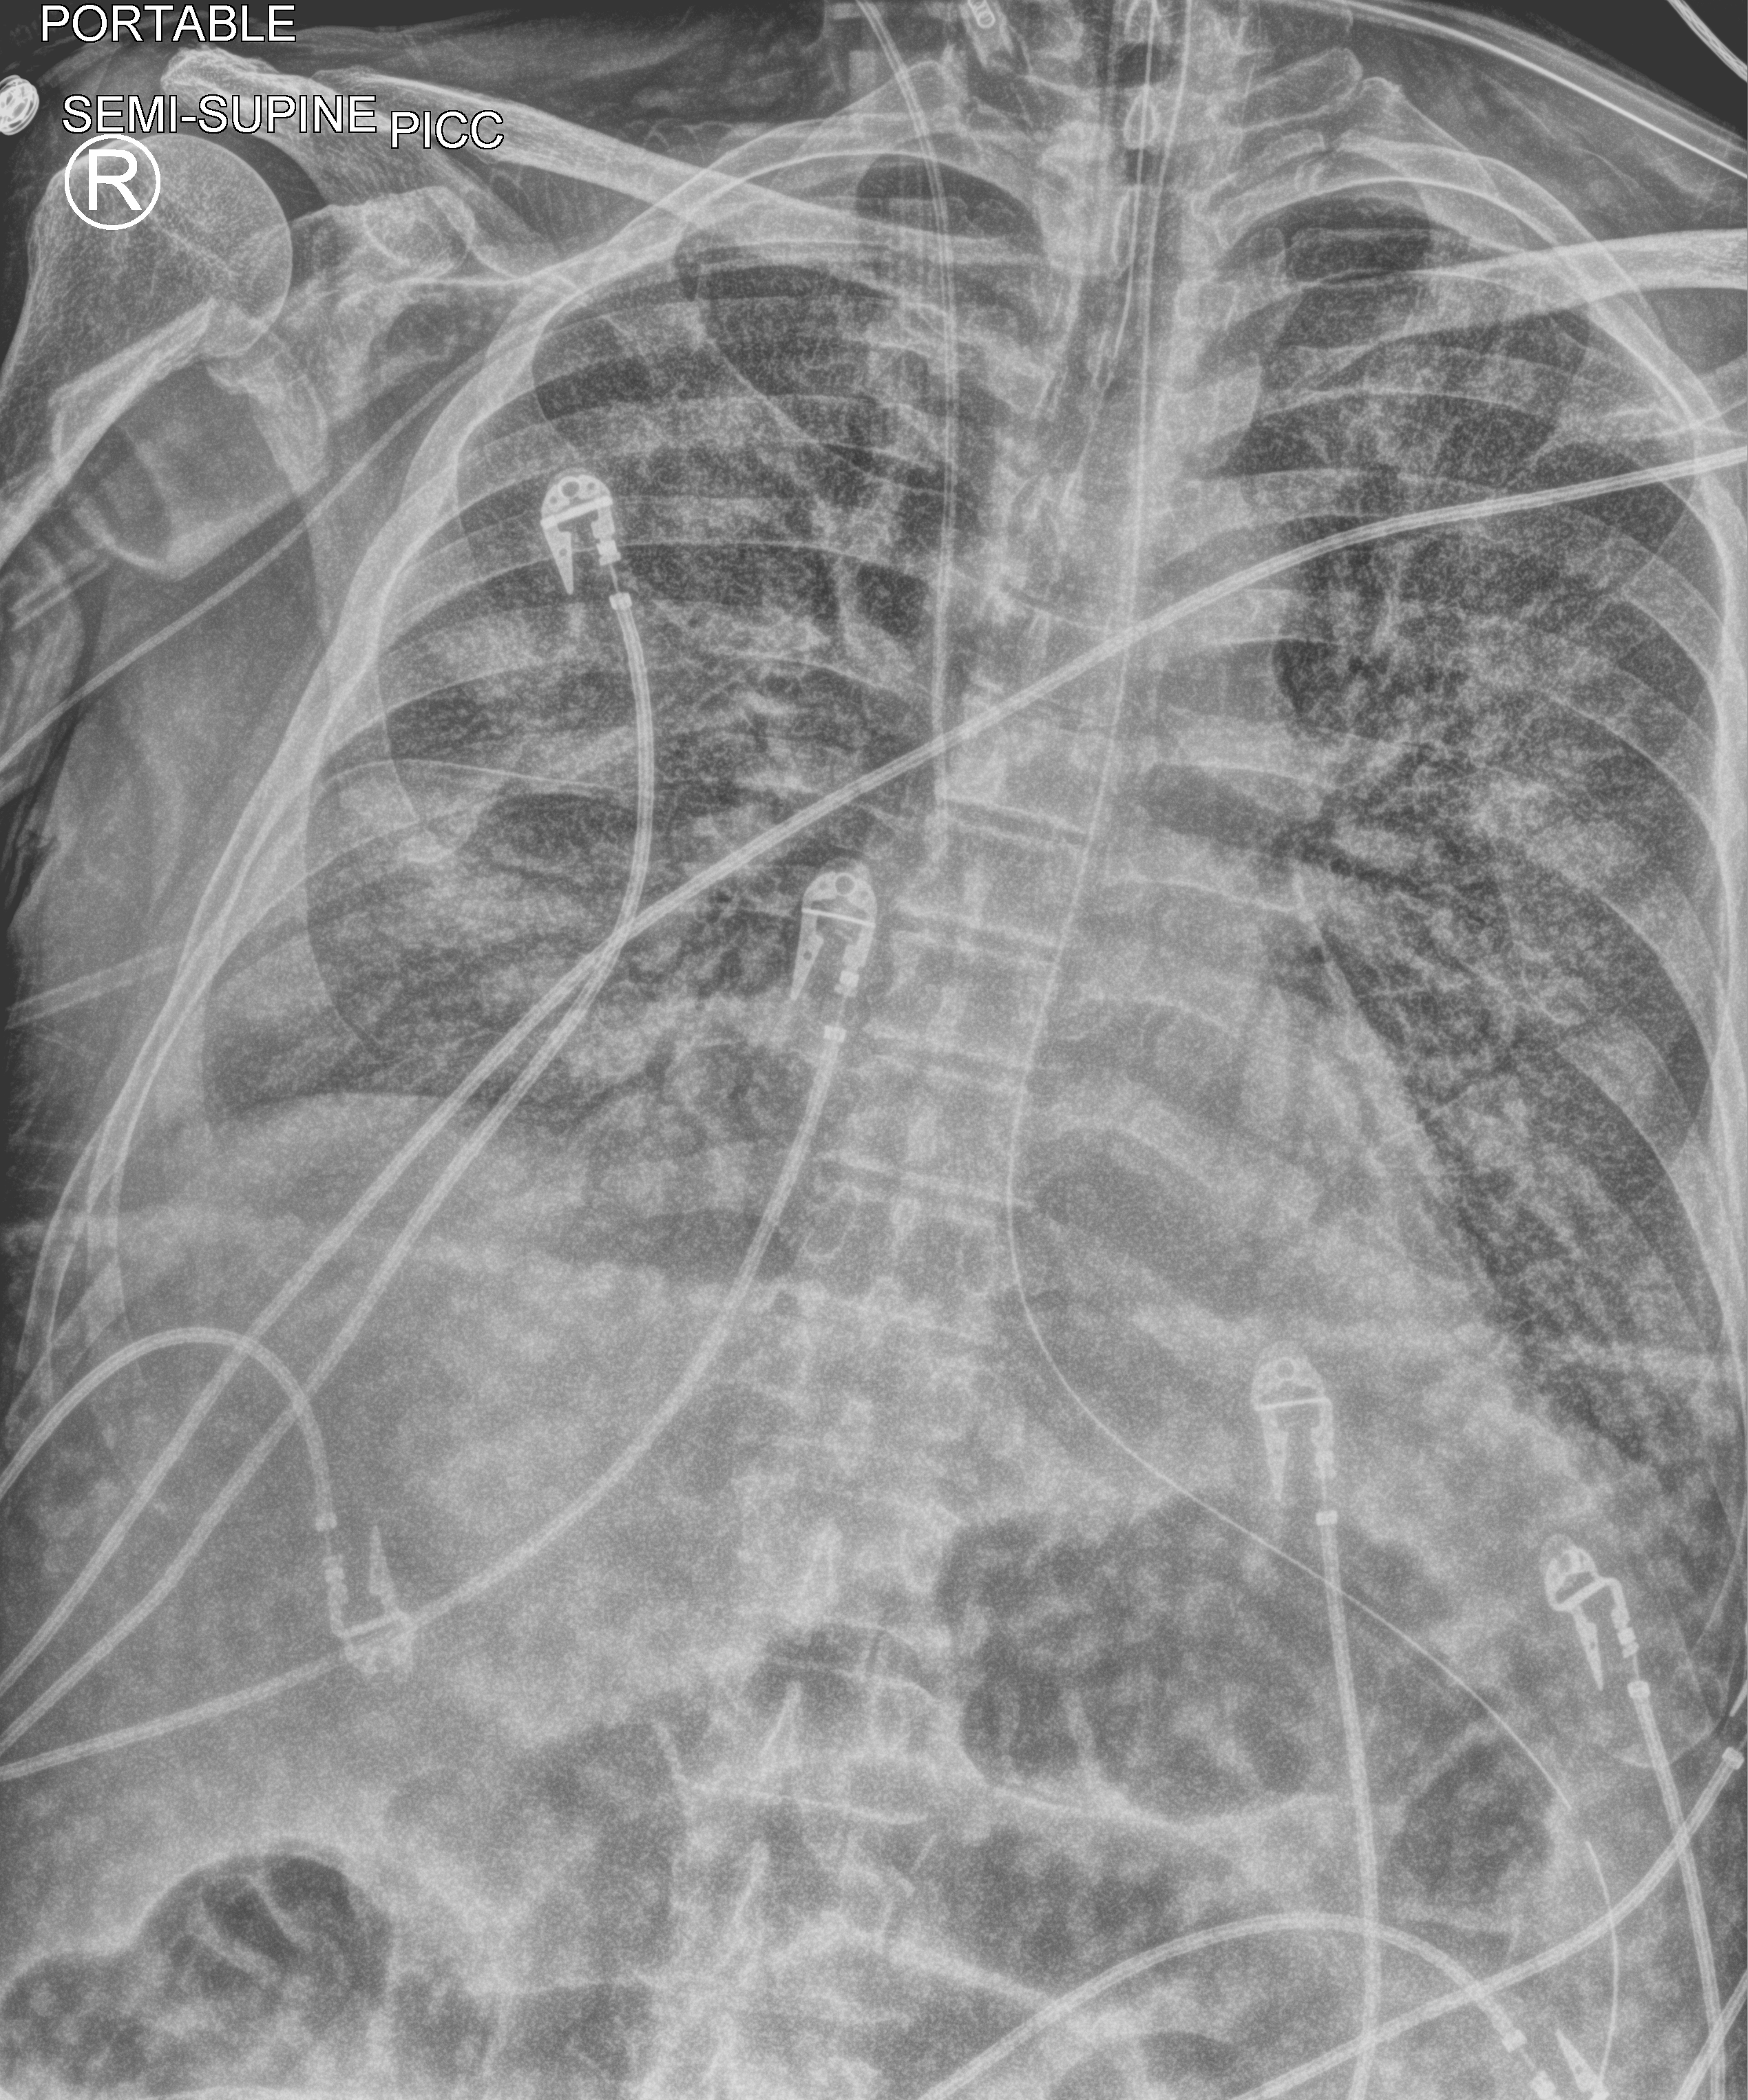
Bedside chest radiograph (computed radiography); anteroposterior (AP) projection. Male patient hospitalised with COVID-19, age 60–74 years.
Admission-level facts for this patient (not findings on this image; timing relative to this image not recorded):
- length of hospital stay: 24 days
- mechanically ventilated during this hospital stay: yes
- admitted to intensive care during this hospital stay: yes